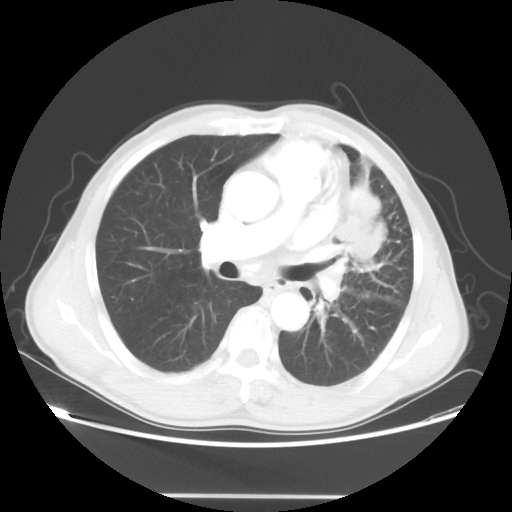
Chest CT, one axial slice; position 29 of 55 along the scan axis; reconstruction kernel STANDARD; lung window (W 1500 / L -600 HU); 512 × 512 image matrix. Patient: male, 60 years. Case-level facts recorded for this patient, not image findings: clinical TNM (as recorded): T3 N3 M0.
Structures marked on this image (bounding box drawn by a radiologist):
- lung tumour (recorded histology: adenocarcinoma): bounding box <348,177,385,265> (left, top, right, bottom; pixels)